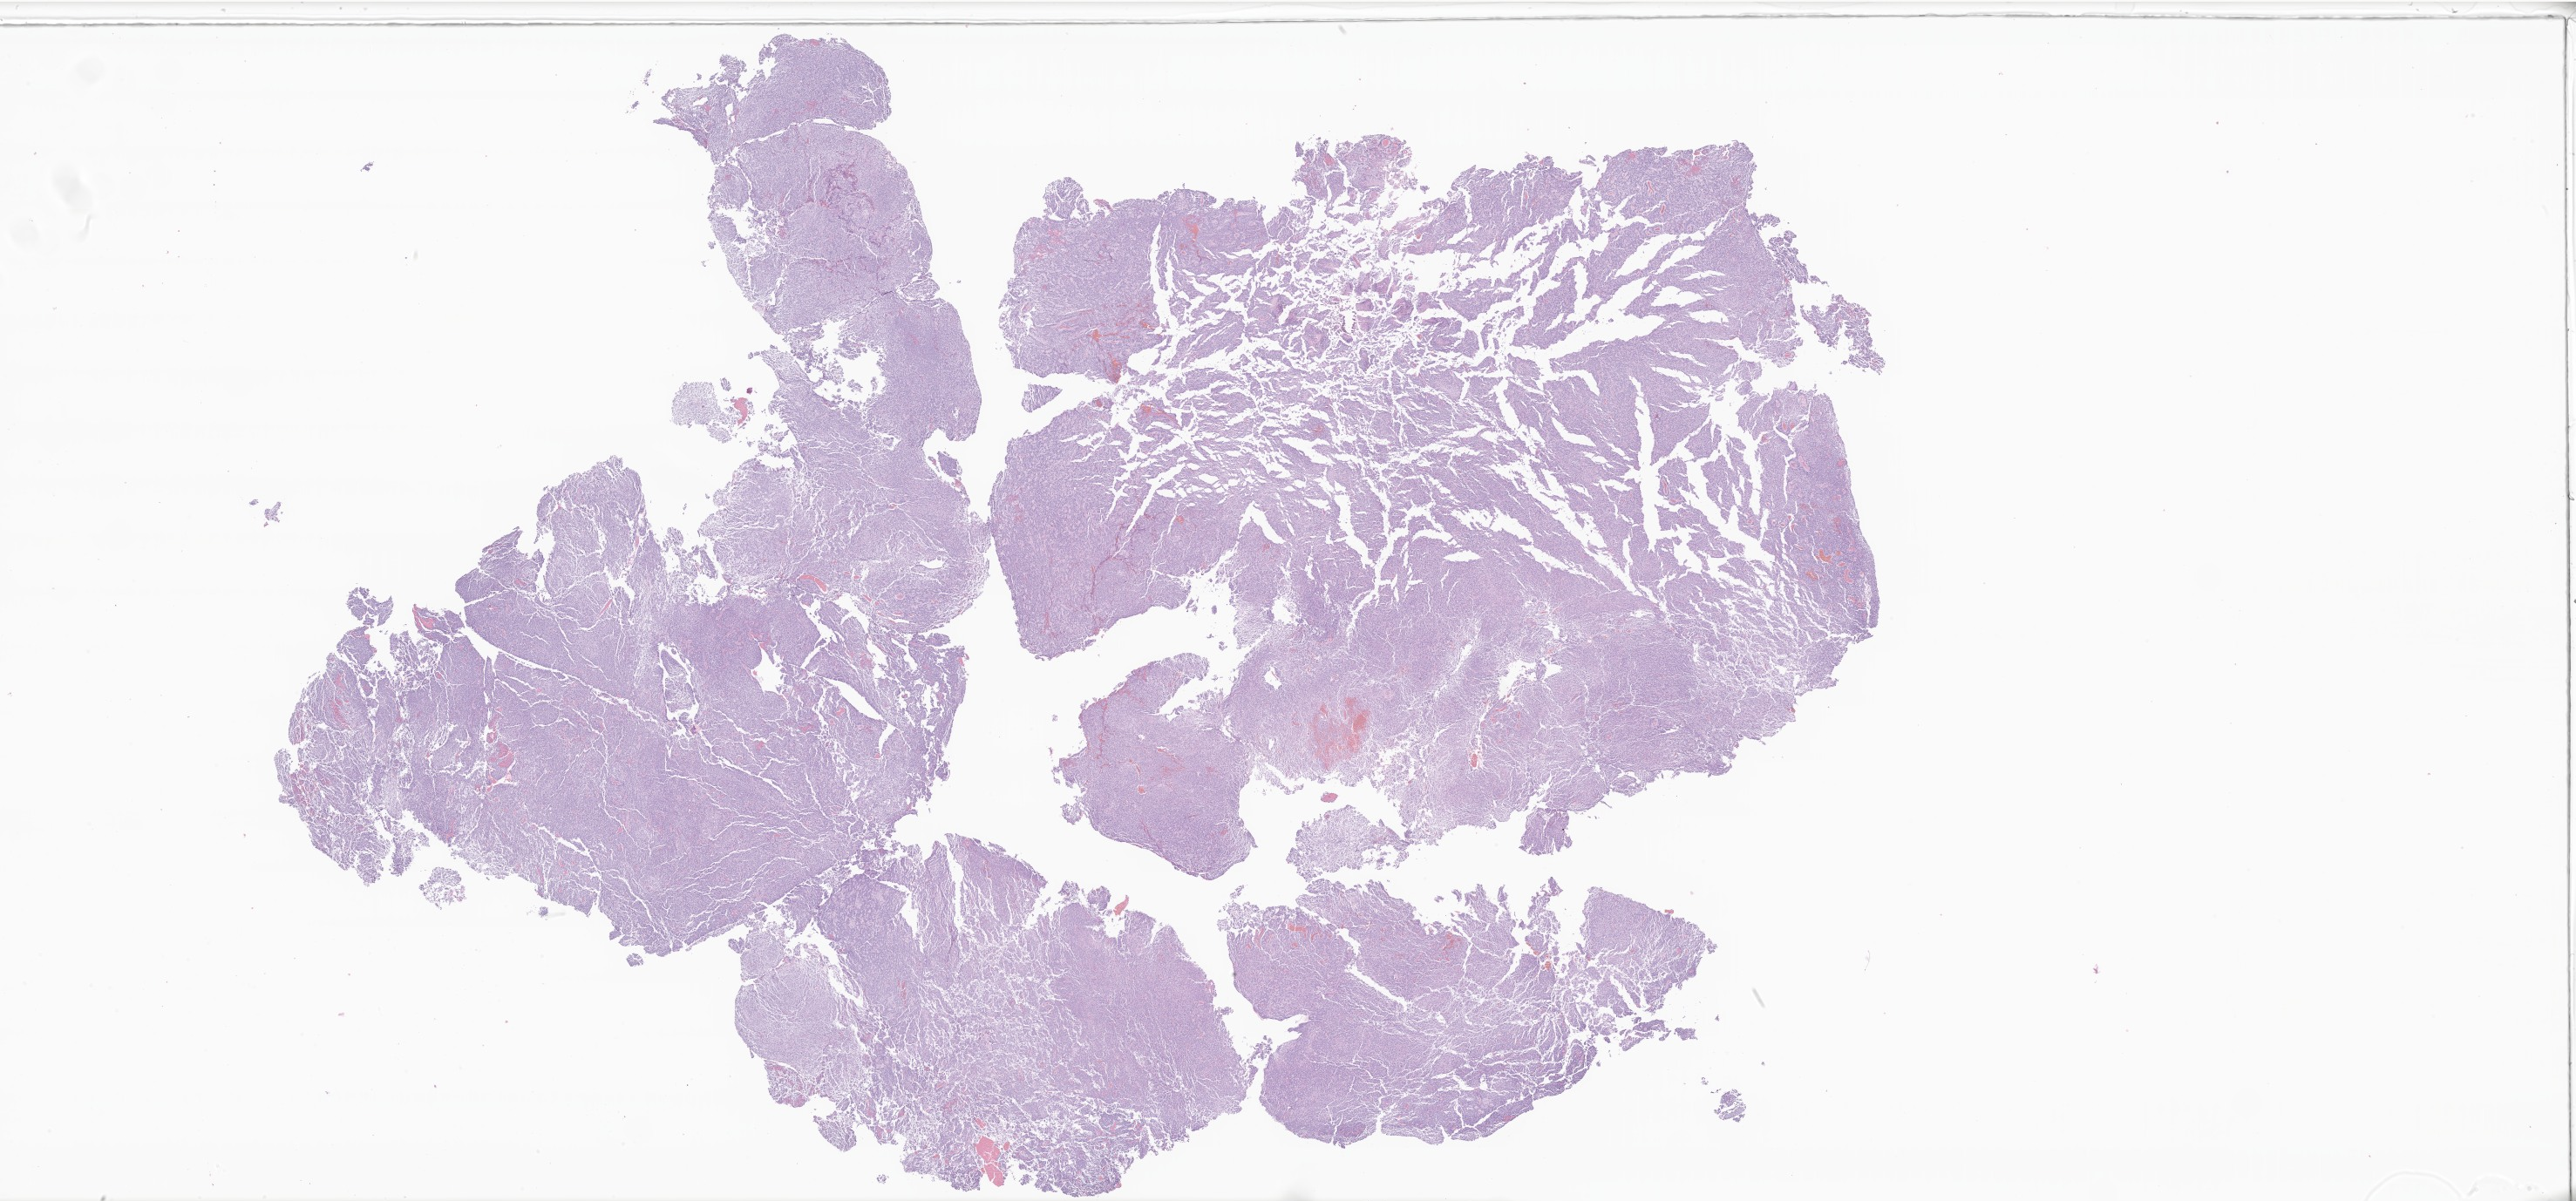
Haematoxylin and eosin whole-slide image of tumor tissue from the cerebral ventricle — a low-resolution overview of the entire scanned area, about 49.8 x 23.2 mm; FFPE section. Male patient, age 119 months (9 years 11 months).
• recorded diagnosis: Medulloblastoma, NOS